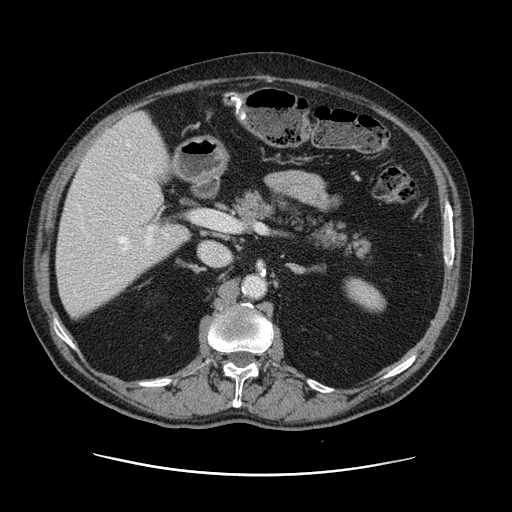
Contrast-enhanced abdominal CT, one axial slice; position 68 of 141 along the scan axis; 120 kVp; intravenous contrast given; soft-tissue window (W 400 / L 40 HU); 512 × 512 image matrix. Male patient, age 72 years. From the clinical record (not read from this slice): diagnosis: colorectal cancer liver metastases, imaged before liver resection; multiple liver metastases: yes; largest metastasis: 5.4 cm; disease in both lobes: yes.
Outlined on this slice (expert manual segmentation):
- hepatic veins: bounding box (x1, y1, x2, y2) in pixels: (118, 140, 146, 251)
- liver: (57, 114, 188, 318)
- planned liver remnant (the part of the liver to remain after resection): (57, 187, 188, 318)
- portal vein (with intrahepatic branches): (81, 211, 203, 247)